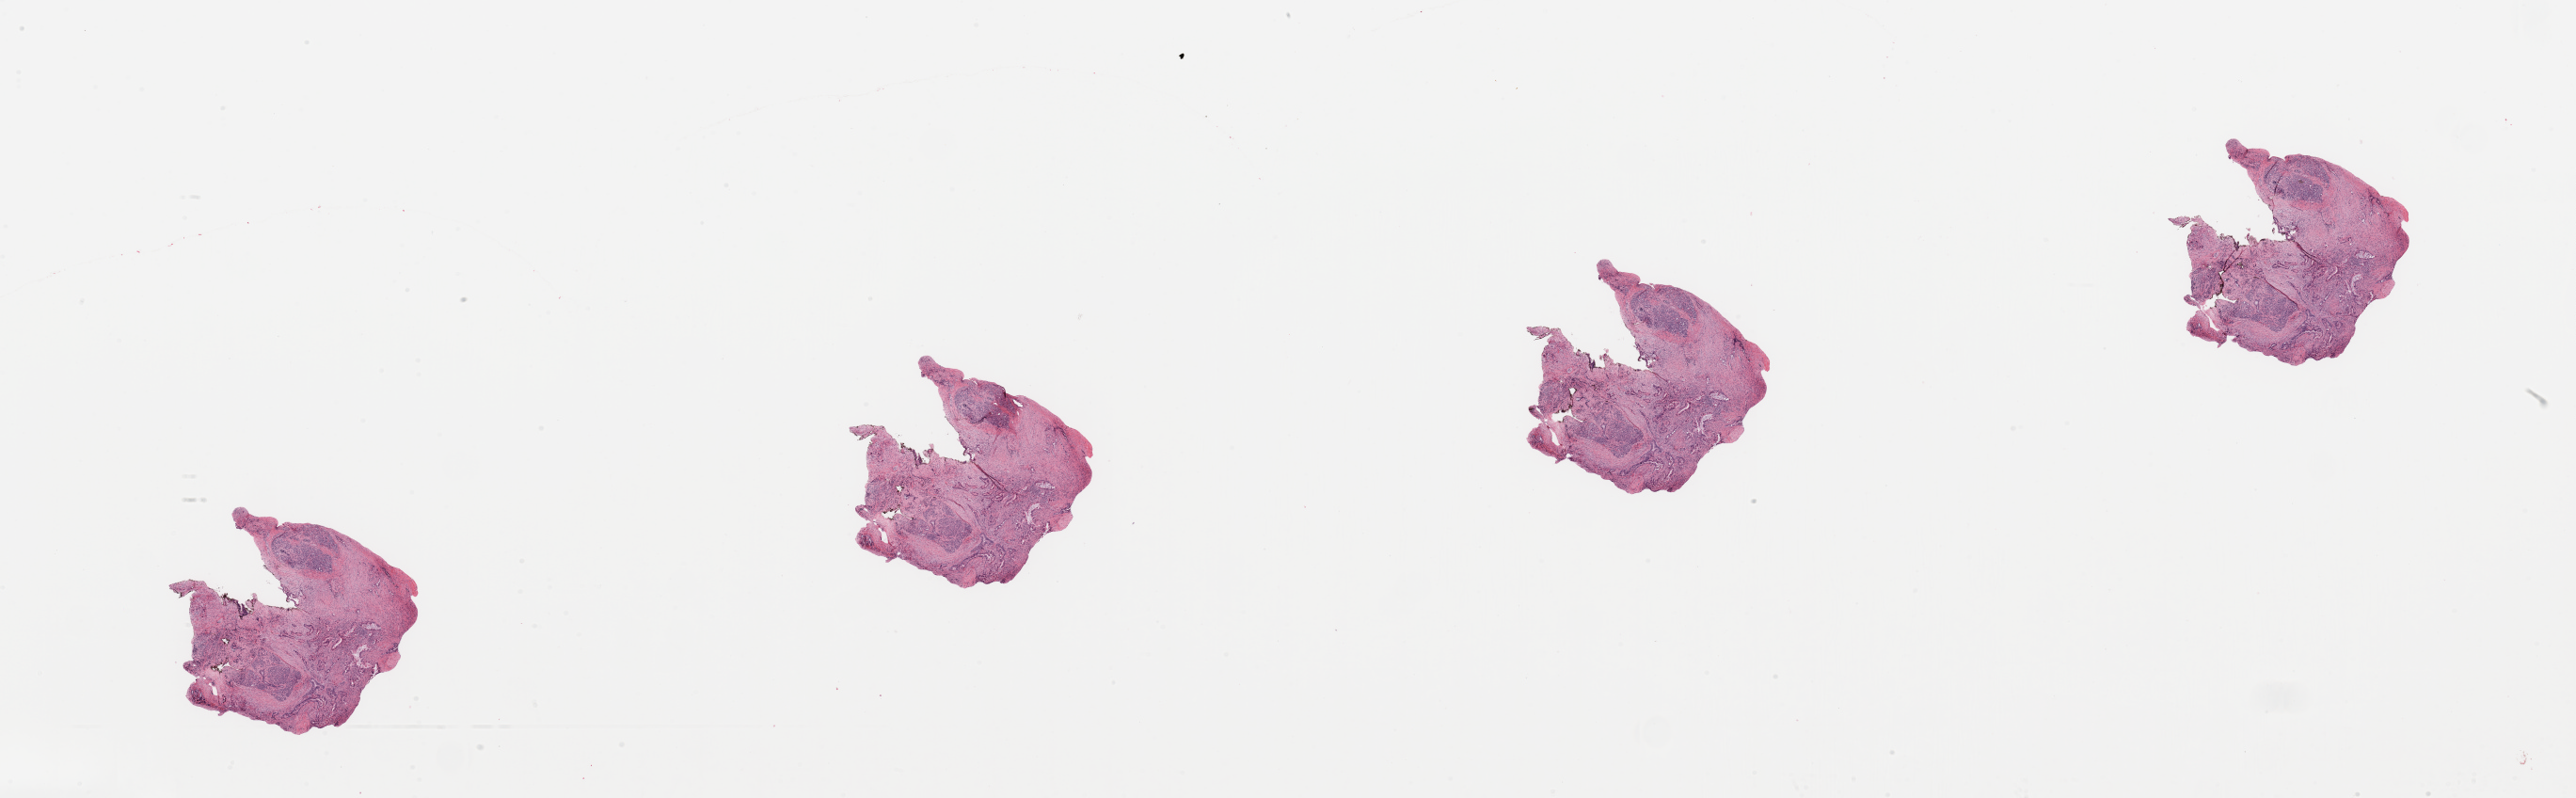
Digitized Hematoxylin and eosin (H&E) stained tissue section (whole slide), a low-resolution overview of the entire scanned area, about 43.3 x 13.4 mm (acquisition: 20x scan). Tumour tissue sample, pancreas. Male, 80 y/o. Histologic grade: G2 (moderately differentiated).
Primary tumour site (as recorded): head. AJCC pathologic stage: IIA. Histologic diagnosis: Infiltrating duct carcinoma, NOS.